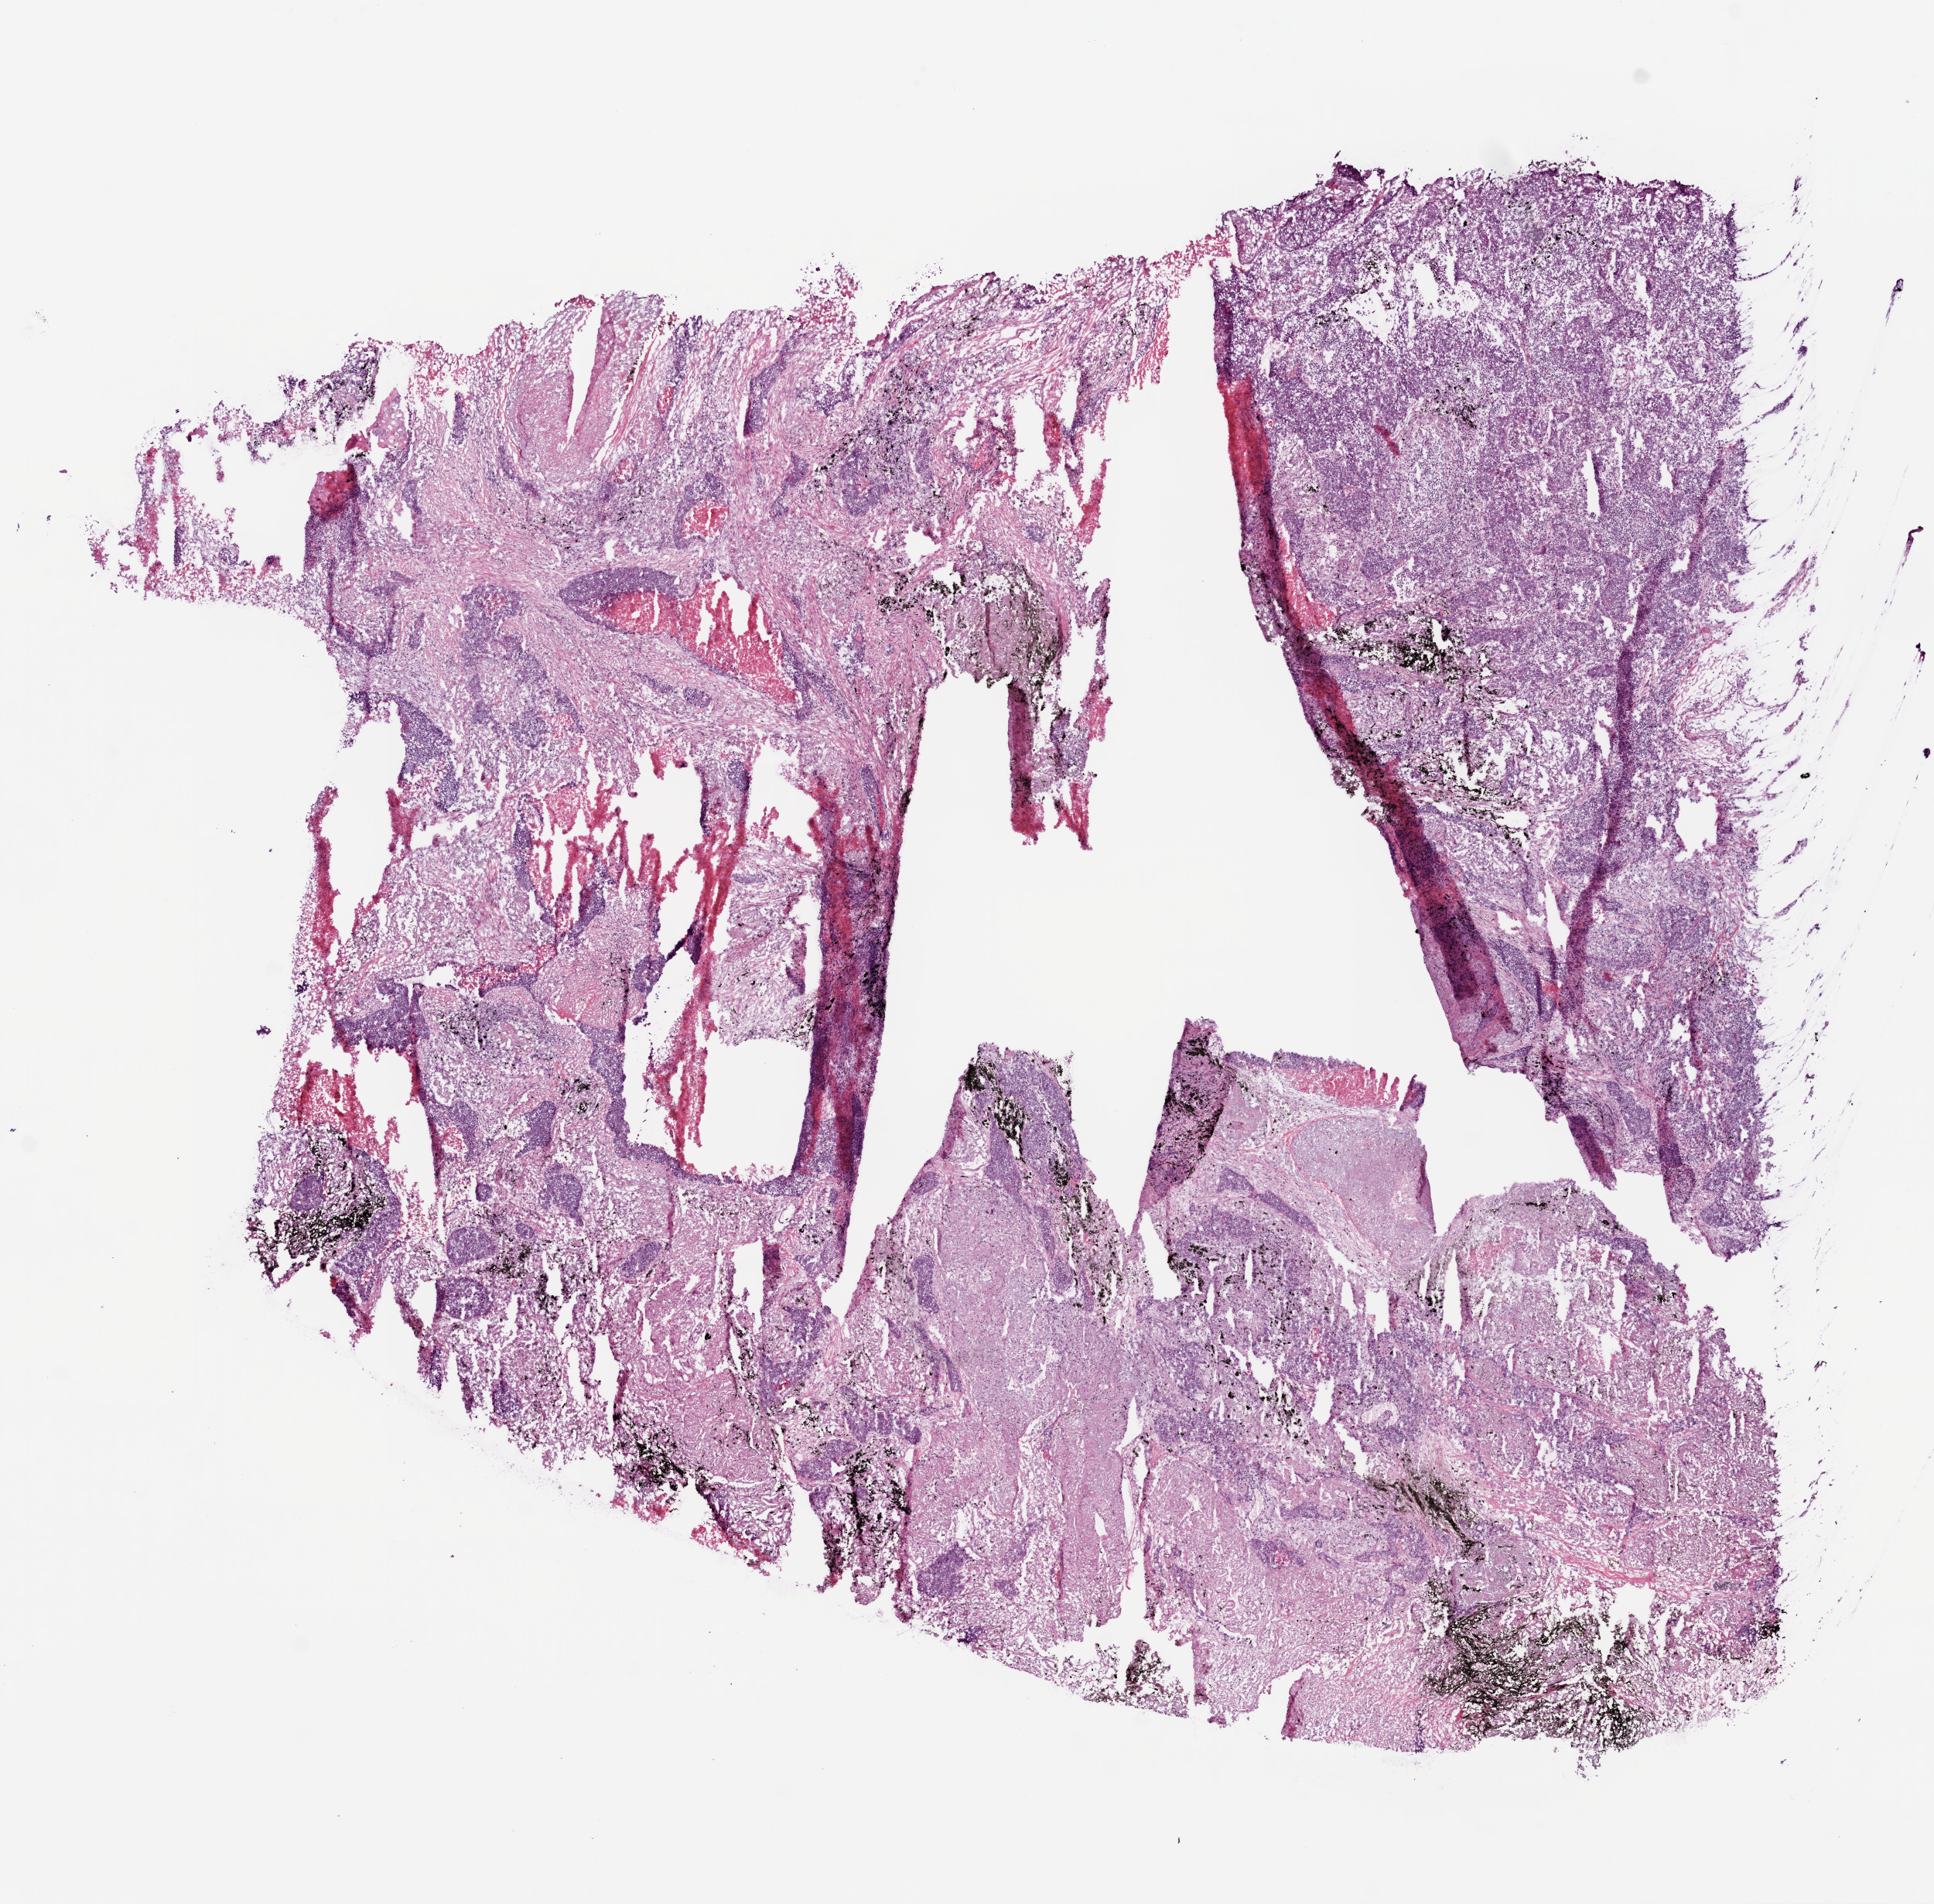
H&E whole-slide image — whole scanned area (about 10.0 x 9.9 mm) shown as a low-resolution overview. Frozen section from the bottom of the tissue portion. Sample: primary tumour, lung. Male patient; age at initial diagnosis 75 years. Composition of this section per pathologist review: tumour cells 55%, tumour nuclei 70%, normal cells 0%, stromal cells 30%, necrosis 15%.
• AJCC pathologic stage: IIIA
• histologic diagnosis: Squamous cell carcinoma, NOS (upper lobe, lung)
• TNM: T4 N0 M0